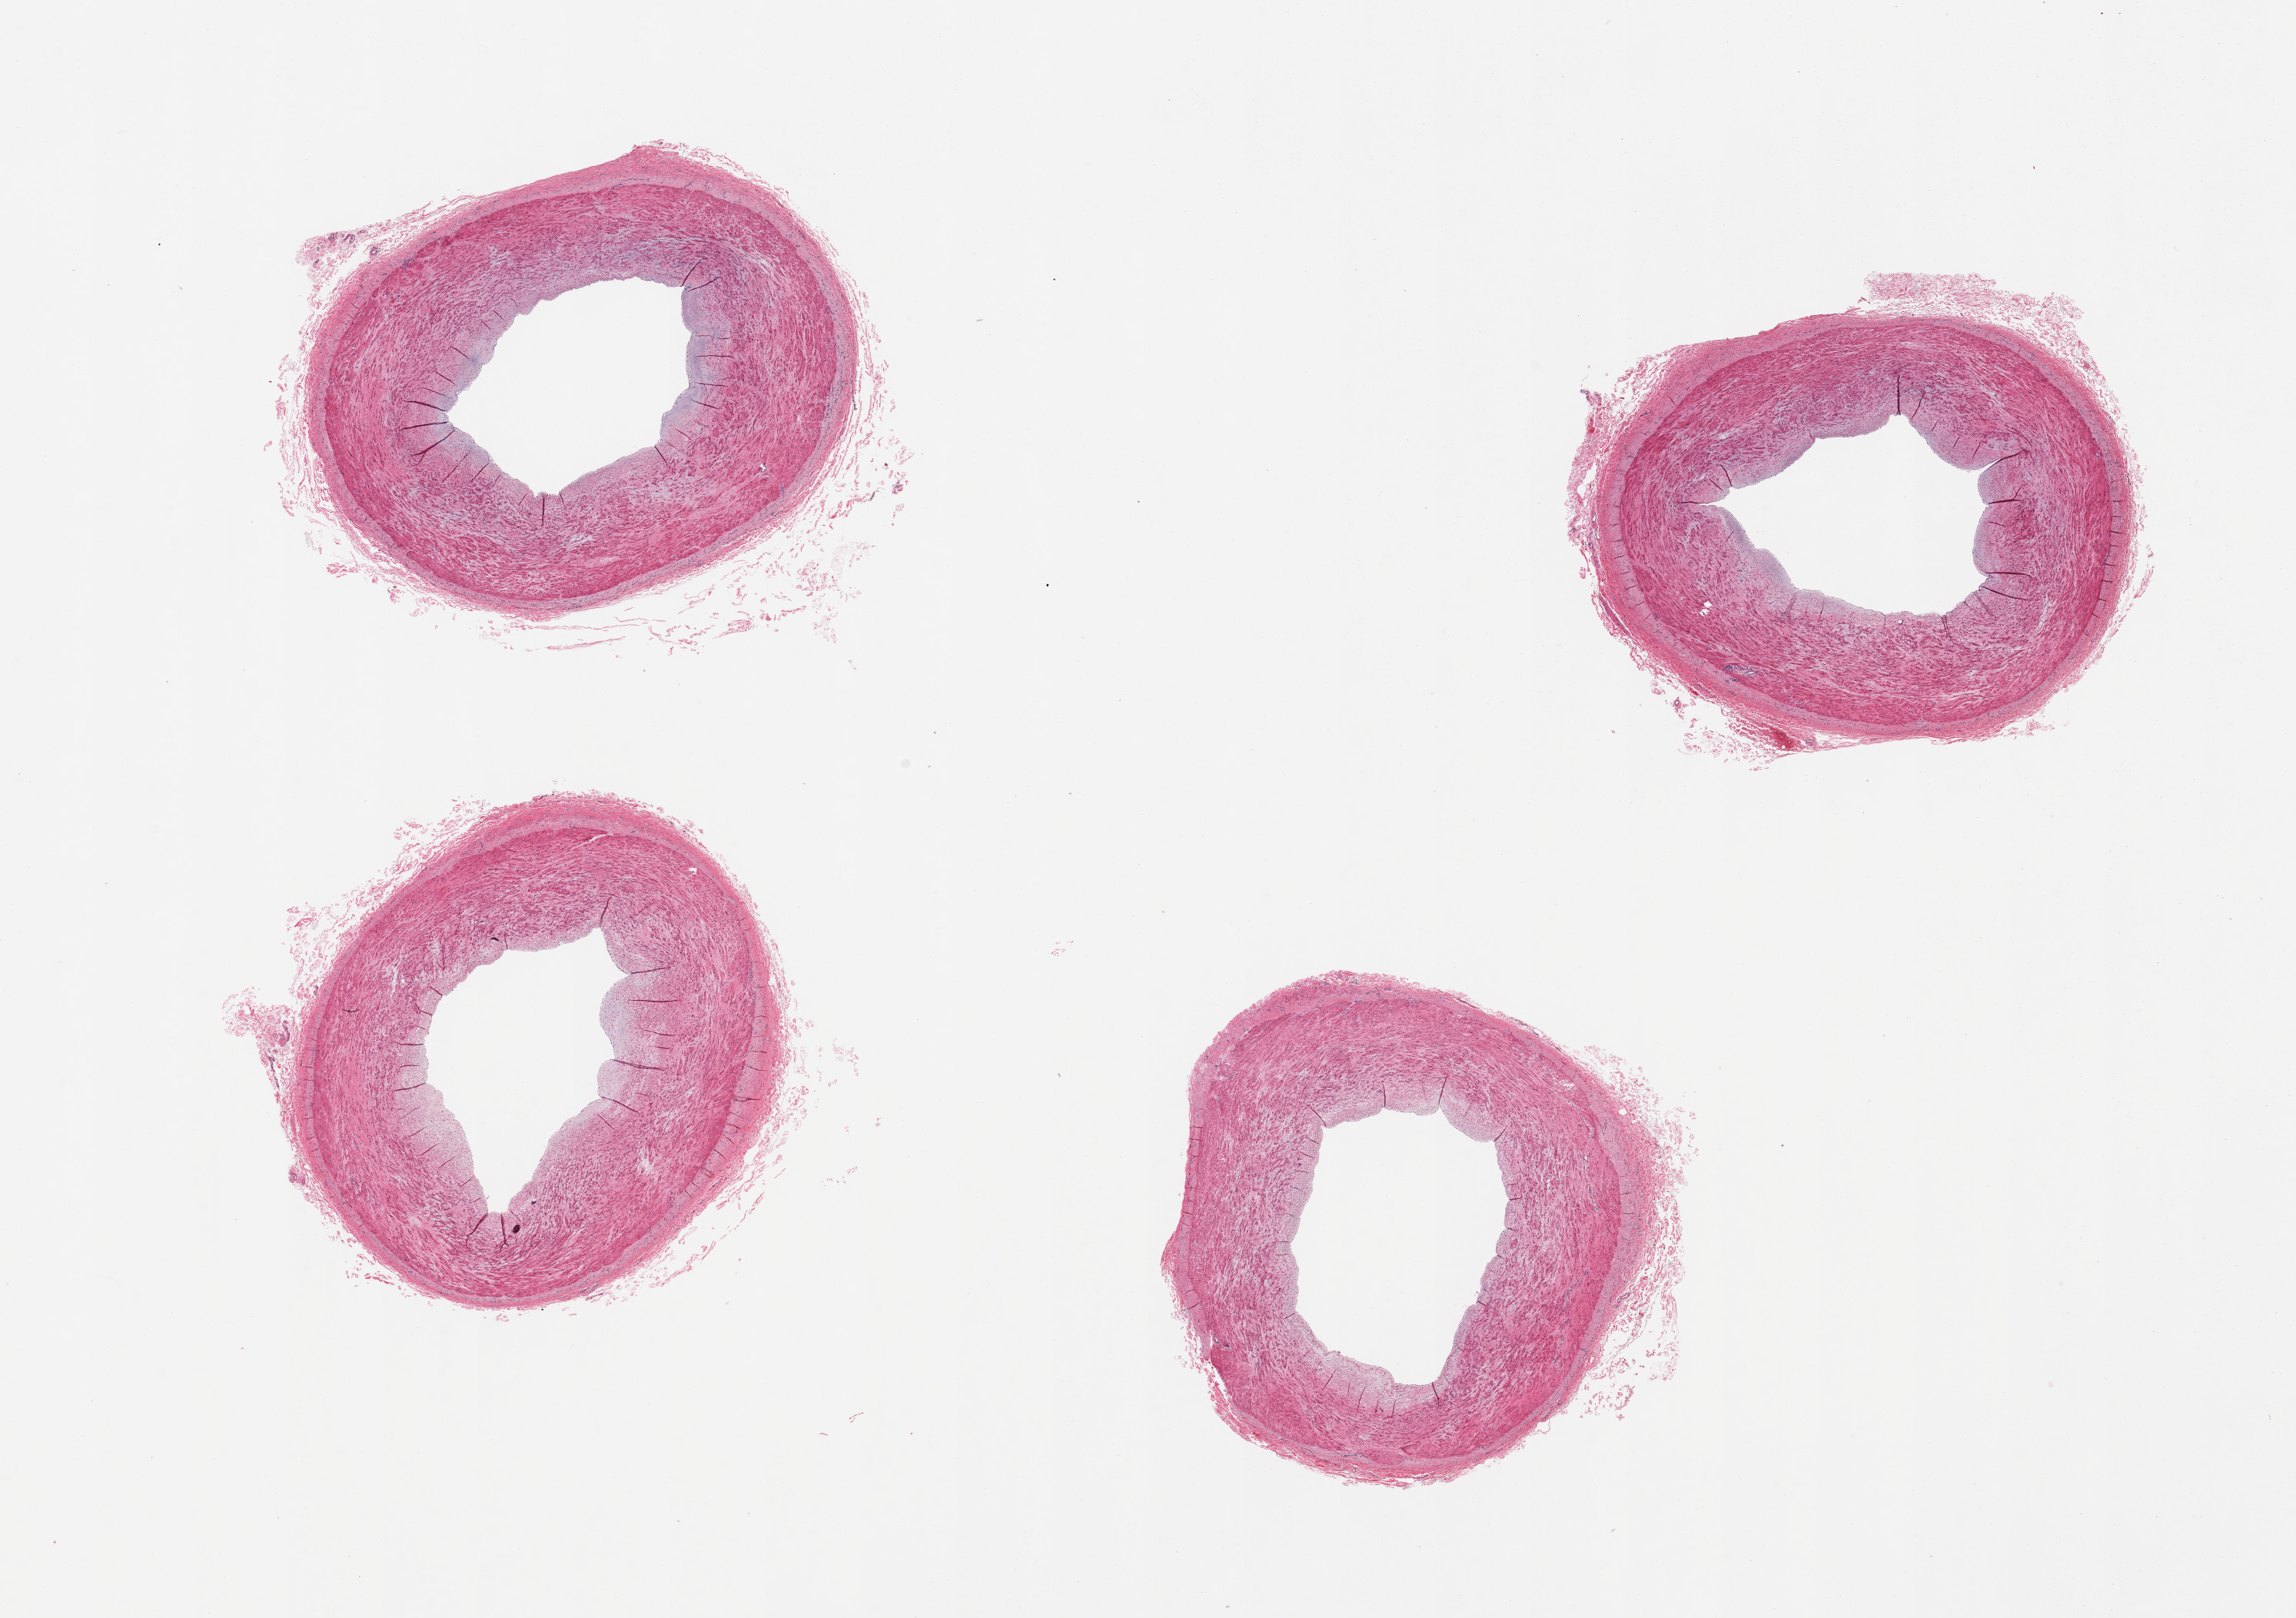
Digitized H&E-stained section, a low-resolution overview of the entire scanned area, about 23.6 x 16.6 mm (slide scanned at 20x); PAXgene-fixed, paraffin-embedded tissue; section of tibial artery (target tissue); donor tissue sample. Donor: male.
• pathologist's review note for this sample: 4 pieces, well-trimmed. Some intimal thickening